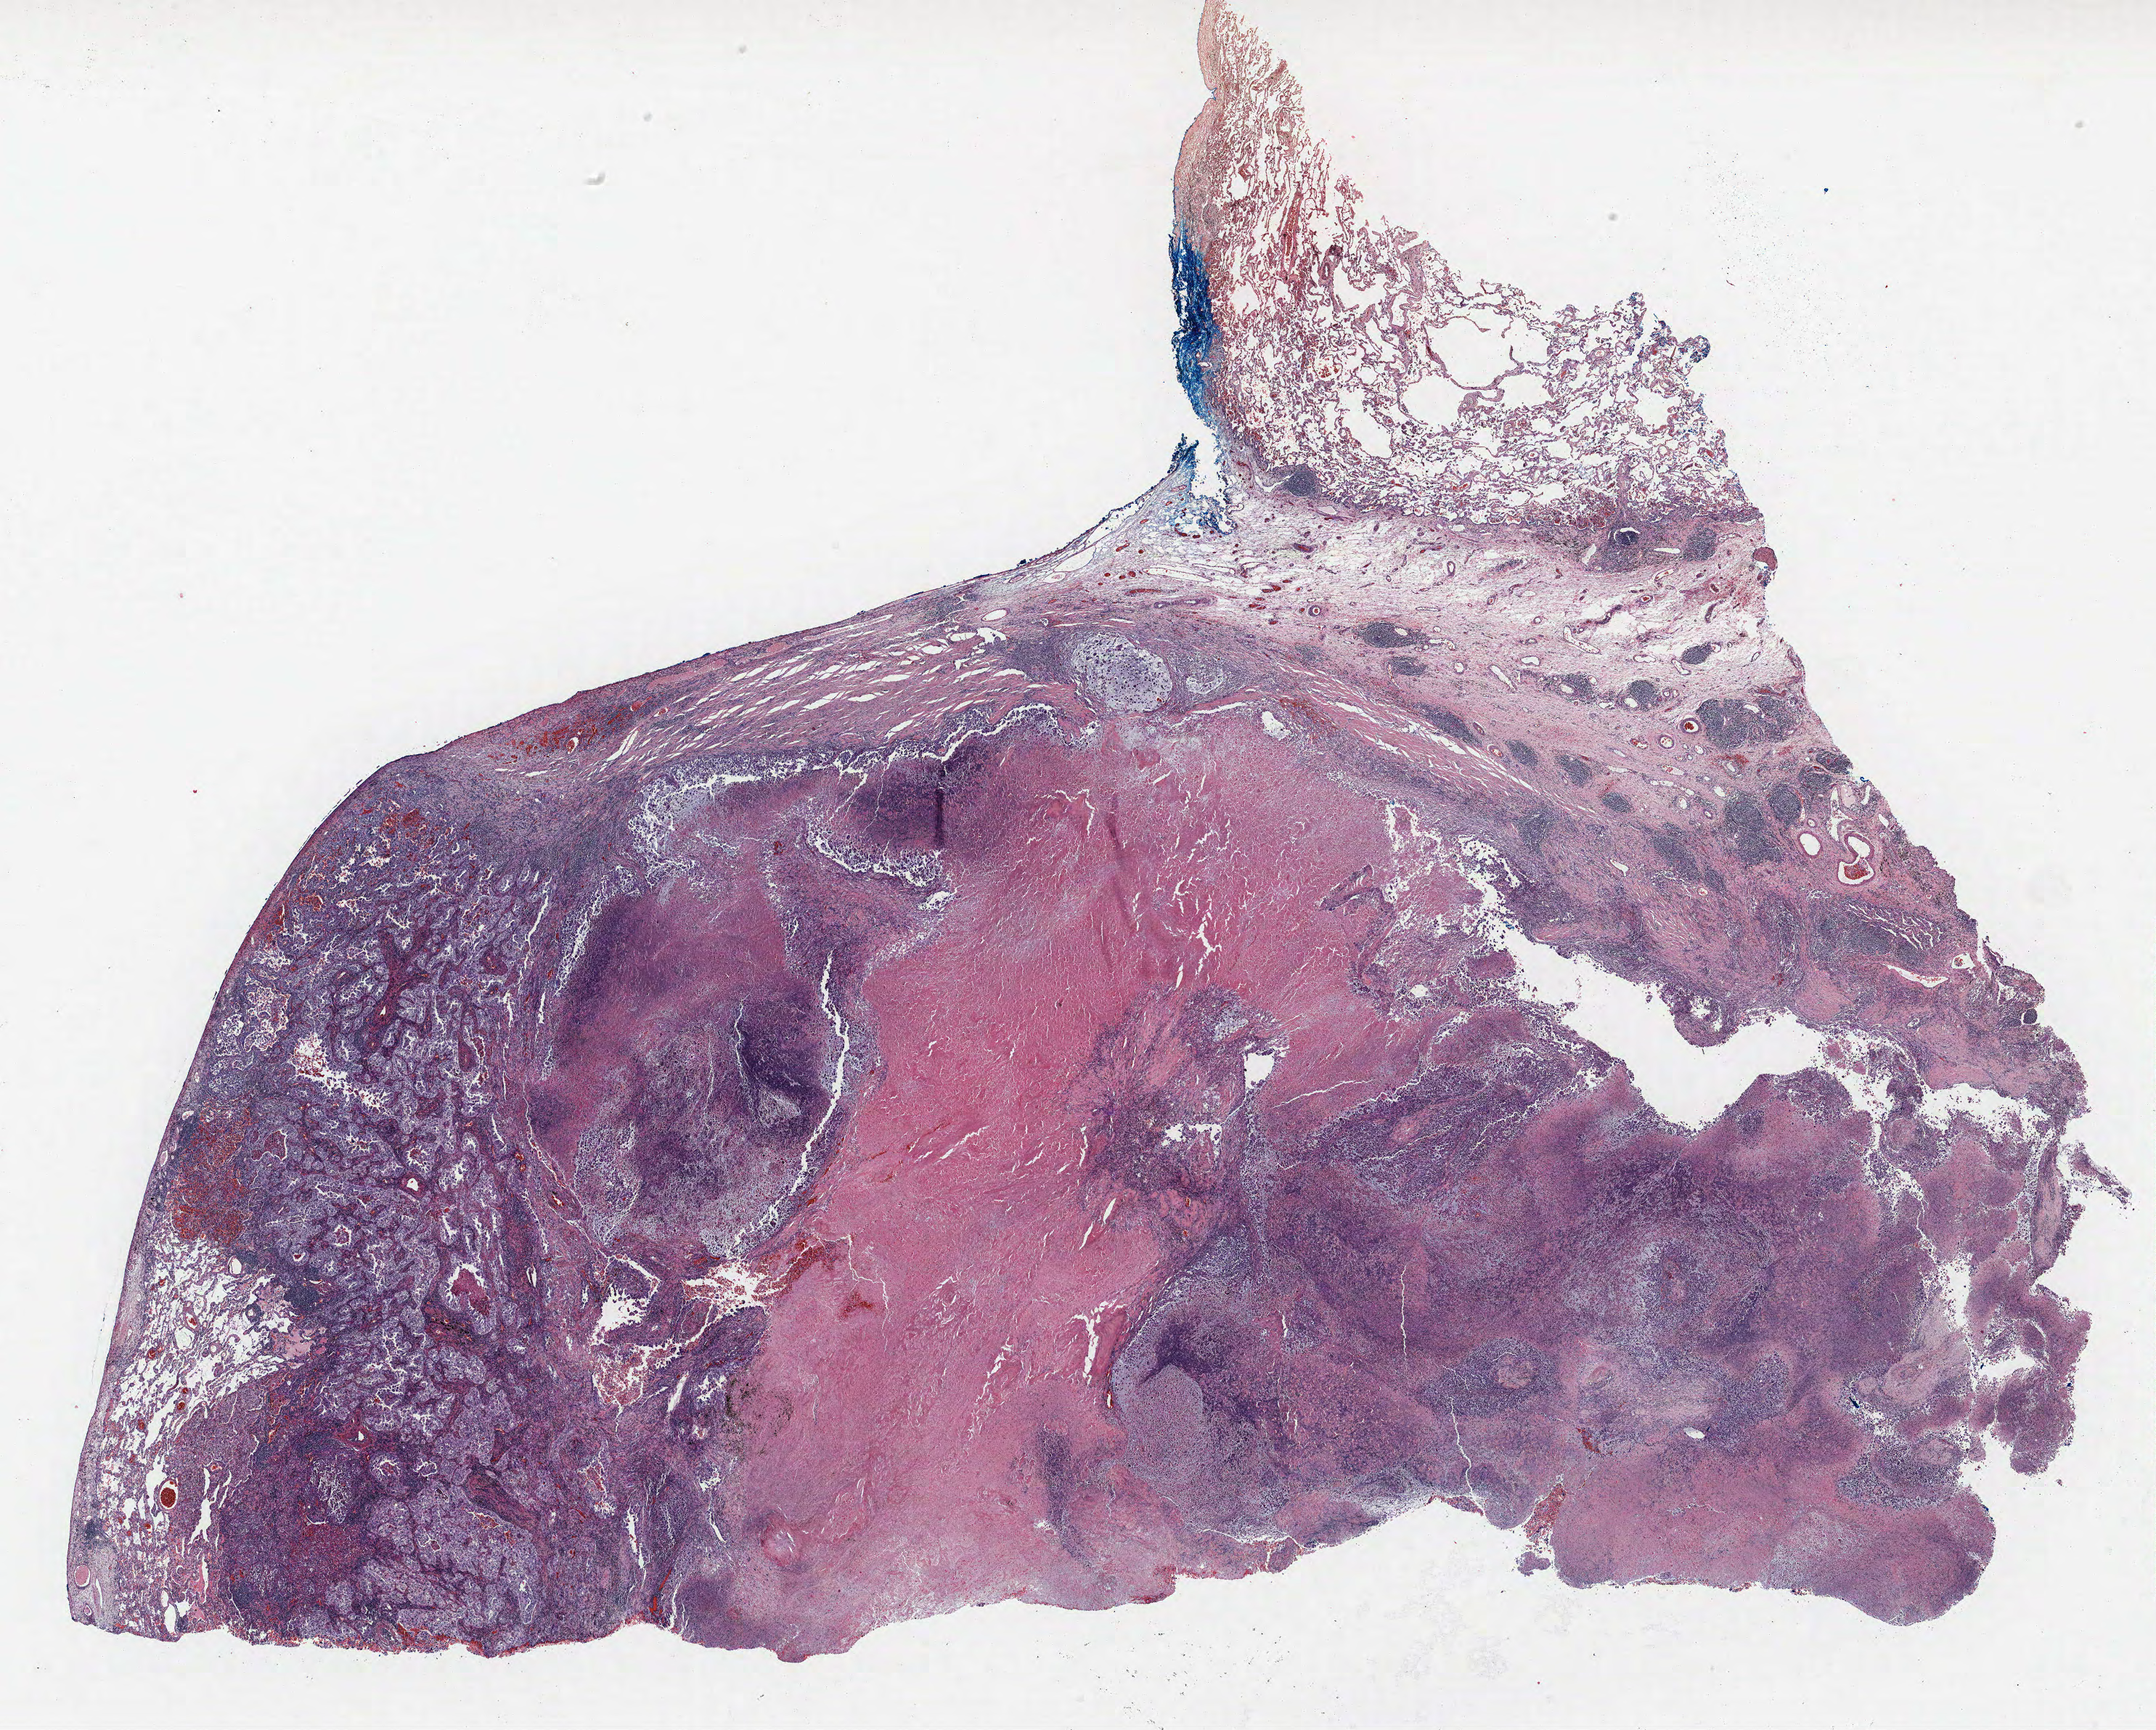
Hematoxylin and eosin (H&E) stained whole-slide image — a low-resolution overview of the entire scanned area, about 23.8 x 19.1 mm (acquisition: 40x scan). FFPE section. Lung tissue. Female patient, aged 64 at enrolment. Current smoker at enrolment. Grade: poorly differentiated (G3).
Primary tumour location (clinical record): left upper lobe, left lower lobe. Tumour size (pathology): 25 mm. Participant's lung-cancer diagnosis: Adenocarcinoma, NOS (ICD-O-3 8140/3). Stage (AJCC 6th edition): IV.